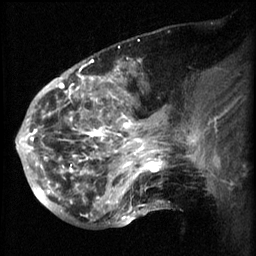
Breast MRI (dynamic contrast-enhanced), one sagittal slice; slice 24 of 60 in the series (ordered by position); 3 images stored at this slice position (order not interpretable as contrast timing); 1.5 T; TE 4.2 ms, TR 8.2 ms; 2.3 mm slice thickness; 256 × 256 image matrix, field of view 200 × 200 mm. Female patient, age 50 years.
Structures marked on this image (semi-automatically segmented with operator editing):
- analysis volume of interest (the breast-tissue region the enhancement analysis was run in; not a lesion): bounding box [x1, y1, x2, y2] px = [50, 64, 169, 217]
- tumour enhancement mask (voxels above the 70 % enhancement threshold inside the analysis volume of interest): [50, 64, 163, 217]